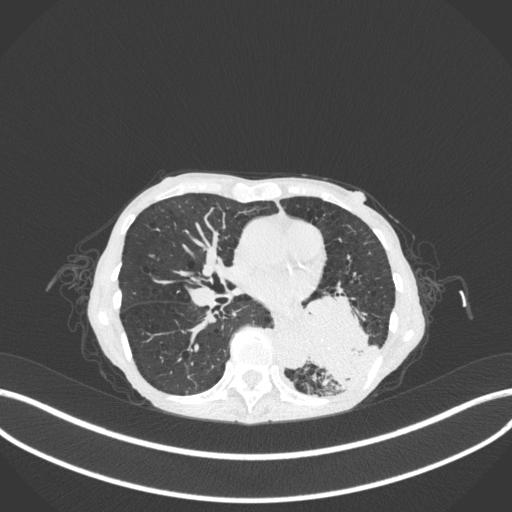
Chest CT, one axial slice; position 131 of 347 along the scan axis; reconstruction kernel B31f; lung window (W 1500 / L -600 HU); 1 mm slice thickness; 512 × 512 image matrix. Female patient, age 70 years. Case-level facts recorded for this patient, not image findings: clinical TNM (as recorded): T3 N0 M0; histopathological grade: G3.
Outlined on this slice (bounding box drawn by a radiologist):
- lung tumour (recorded histology: small cell carcinoma): box from (x=288, y=280) to (x=380, y=386) px